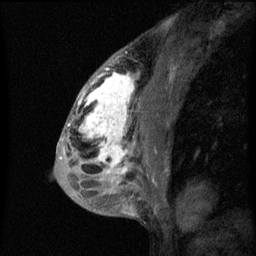
Breast MRI (dynamic contrast-enhanced), one sagittal slice. Position 34 of 60 along the scan axis. Dynamic contrast-enhanced series, image 2 of 3 at this slice position (ordered by acquisition). 1.5 T. TE 4.2 ms, TR 8 ms. 2 mm slice thickness. 256 × 256 image matrix, field of view 180 × 180 mm. Female patient, age 50 years.
Outlined on this slice (semi-automatic segmentation, software-assisted and operator-edited):
- analysis volume of interest (the breast-tissue region the enhancement analysis was run in; not a lesion): bounding box [x1, y1, x2, y2] px = [66, 64, 141, 187]
- tumour enhancement mask (voxels above the 70 % enhancement threshold inside the analysis volume of interest): [67, 64, 134, 175]